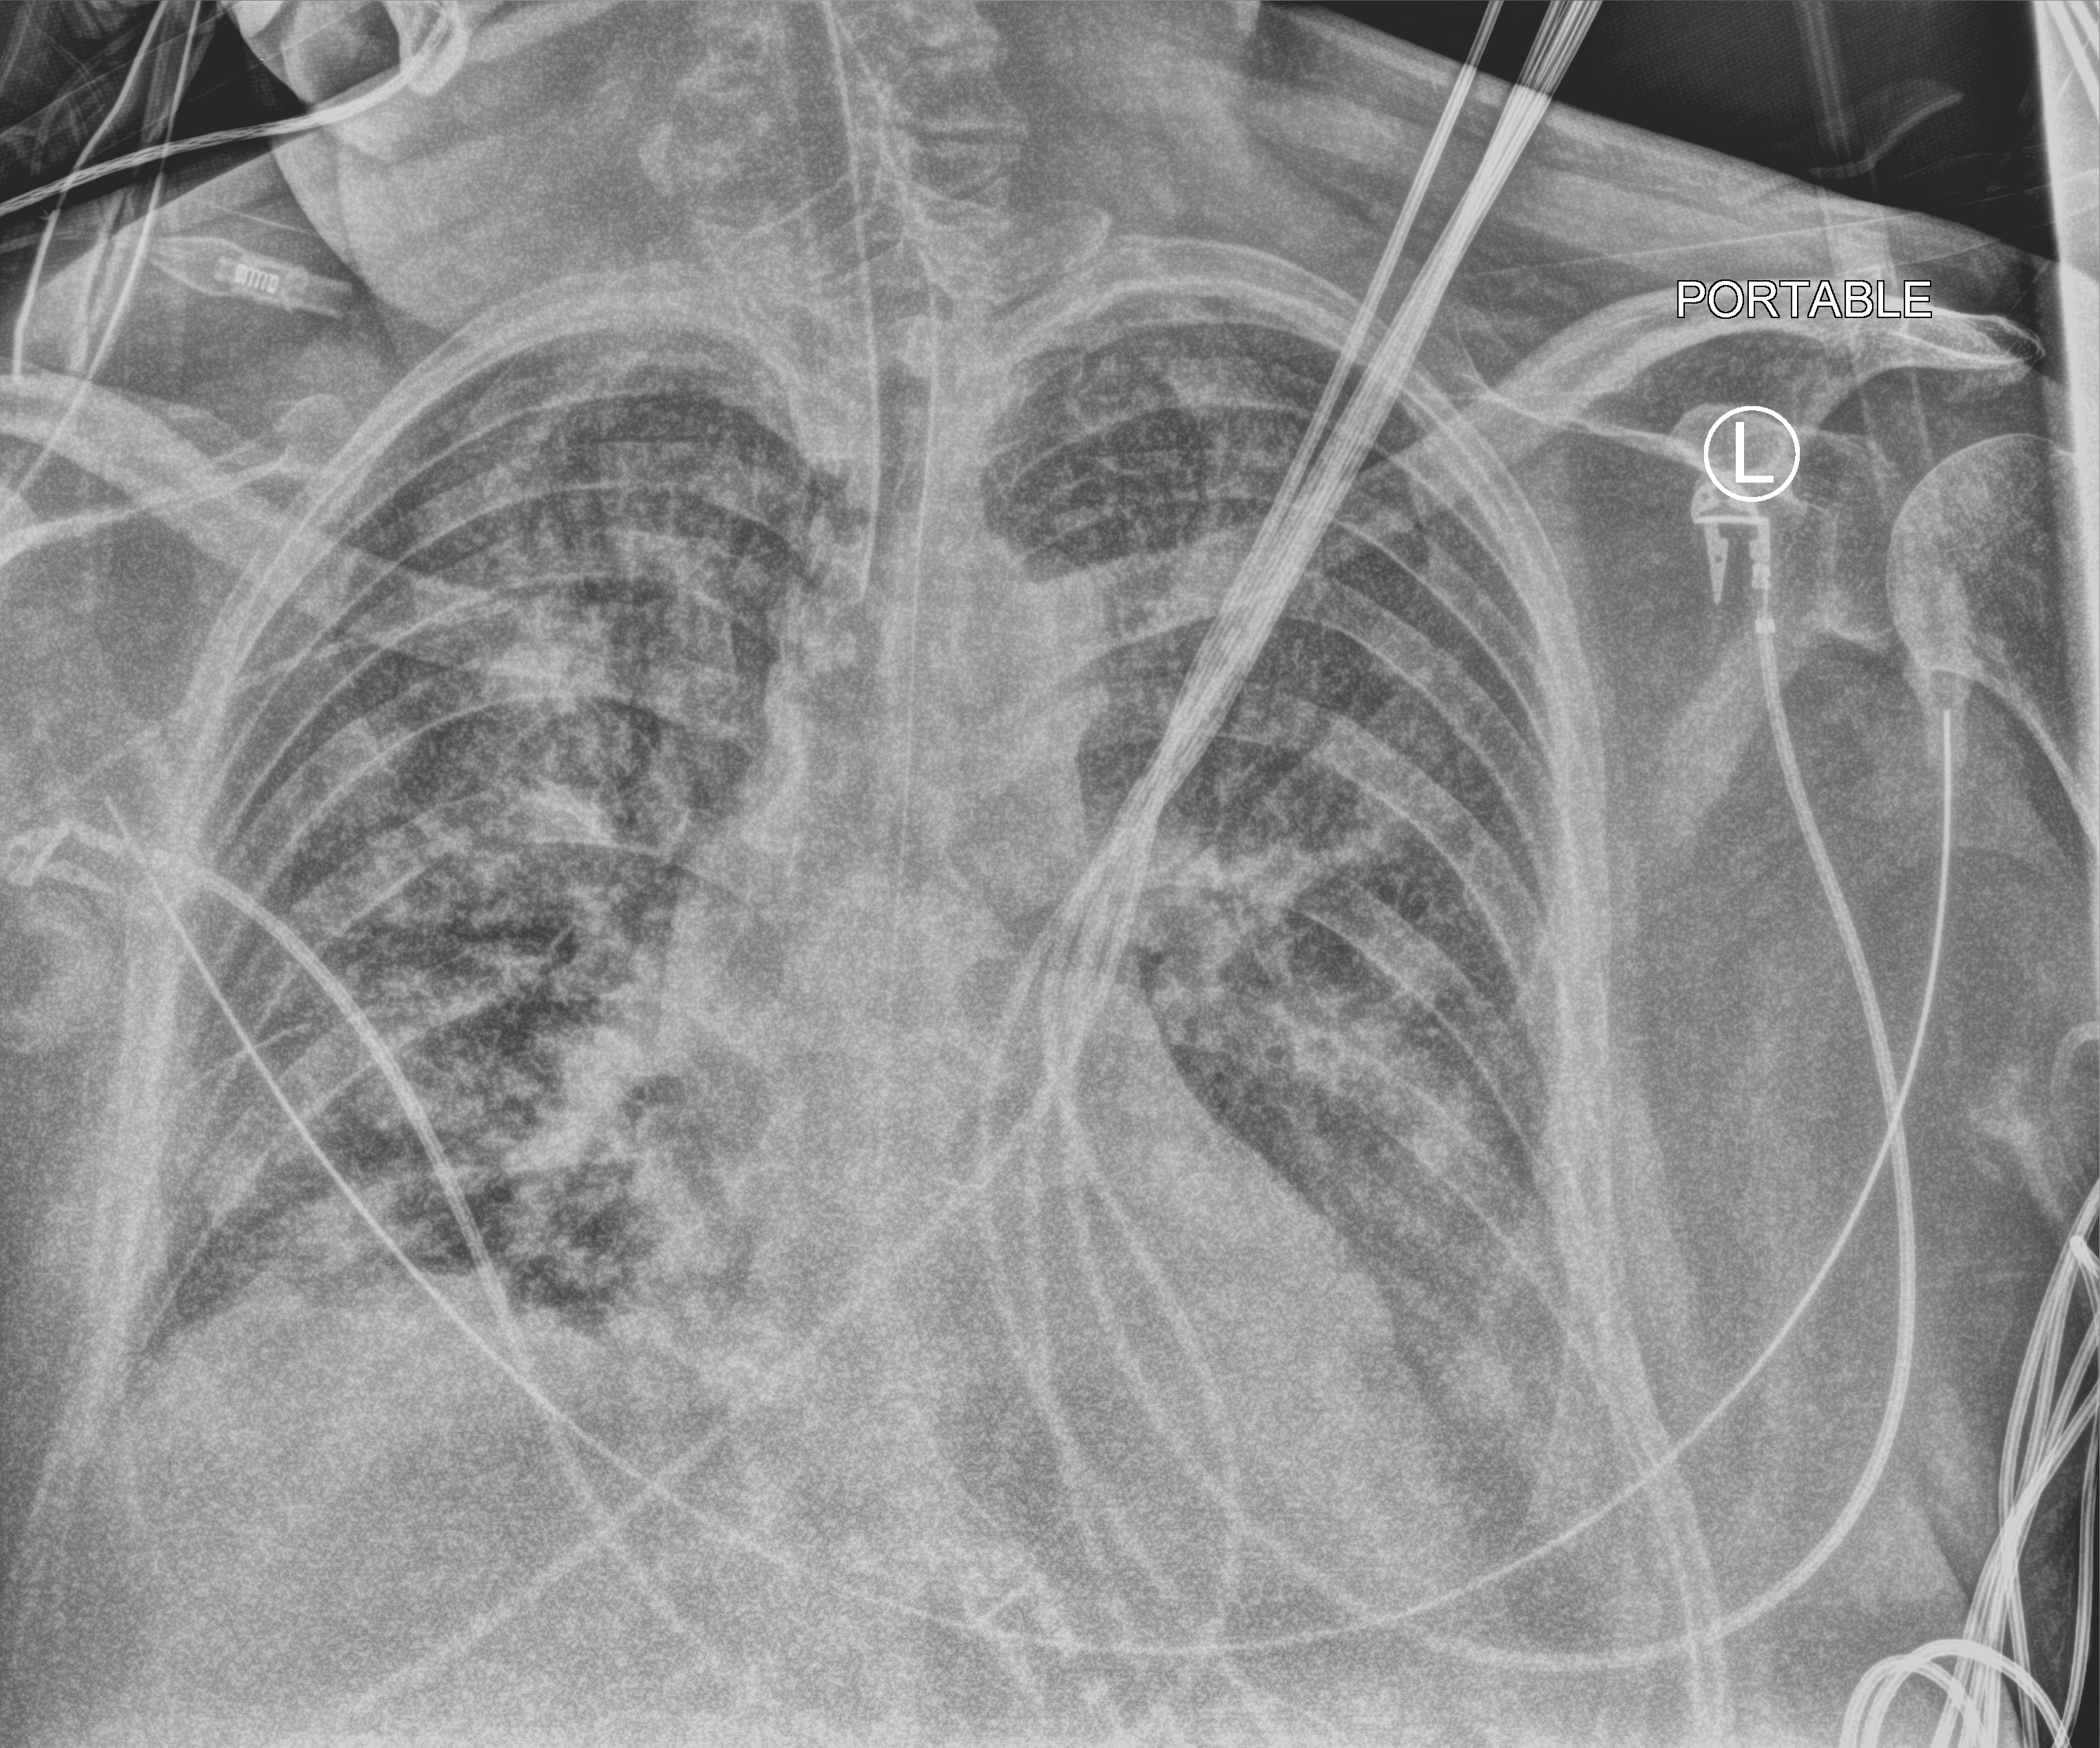
Chest X-ray (portable); anteroposterior (AP) projection. Patient hospitalised with COVID-19; male, aged 60–74 years.
From the hospital-stay record, not from the radiograph (when in the stay this image was taken is not recorded): mechanically ventilated during this hospital stay: yes; length of hospital stay: 20 days; admitted to intensive care during this hospital stay: yes.